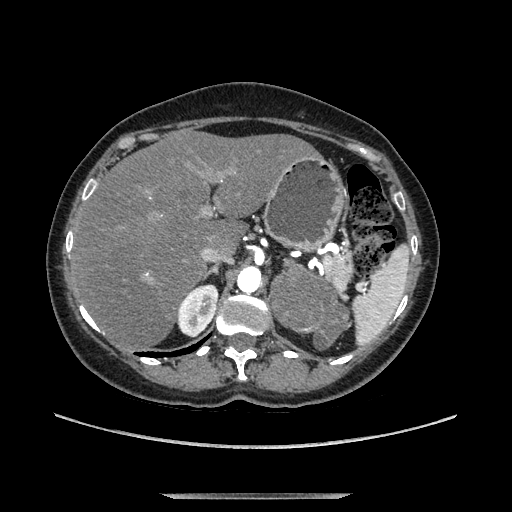
Contrast-enhanced abdominal CT, one axial slice; position 88 of 169 along the scan axis; soft-tissue window (W 400 / L 40 HU); 1.25 mm slice thickness; 512 × 512 image matrix, field of view 400 × 400 mm. Female patient. From the clinical record (not read from this slice): diagnosis: adrenocortical carcinoma; tumour side: left adrenal; tumour size at pathology: 9 cm; Ki-67 index: 2 %; stage (as recorded): 3.
Annotated regions visible in this slice (semi-automatically segmented with operator editing):
- mass: bounding box (x1, y1, x2, y2) in pixels: (274, 264, 346, 346)